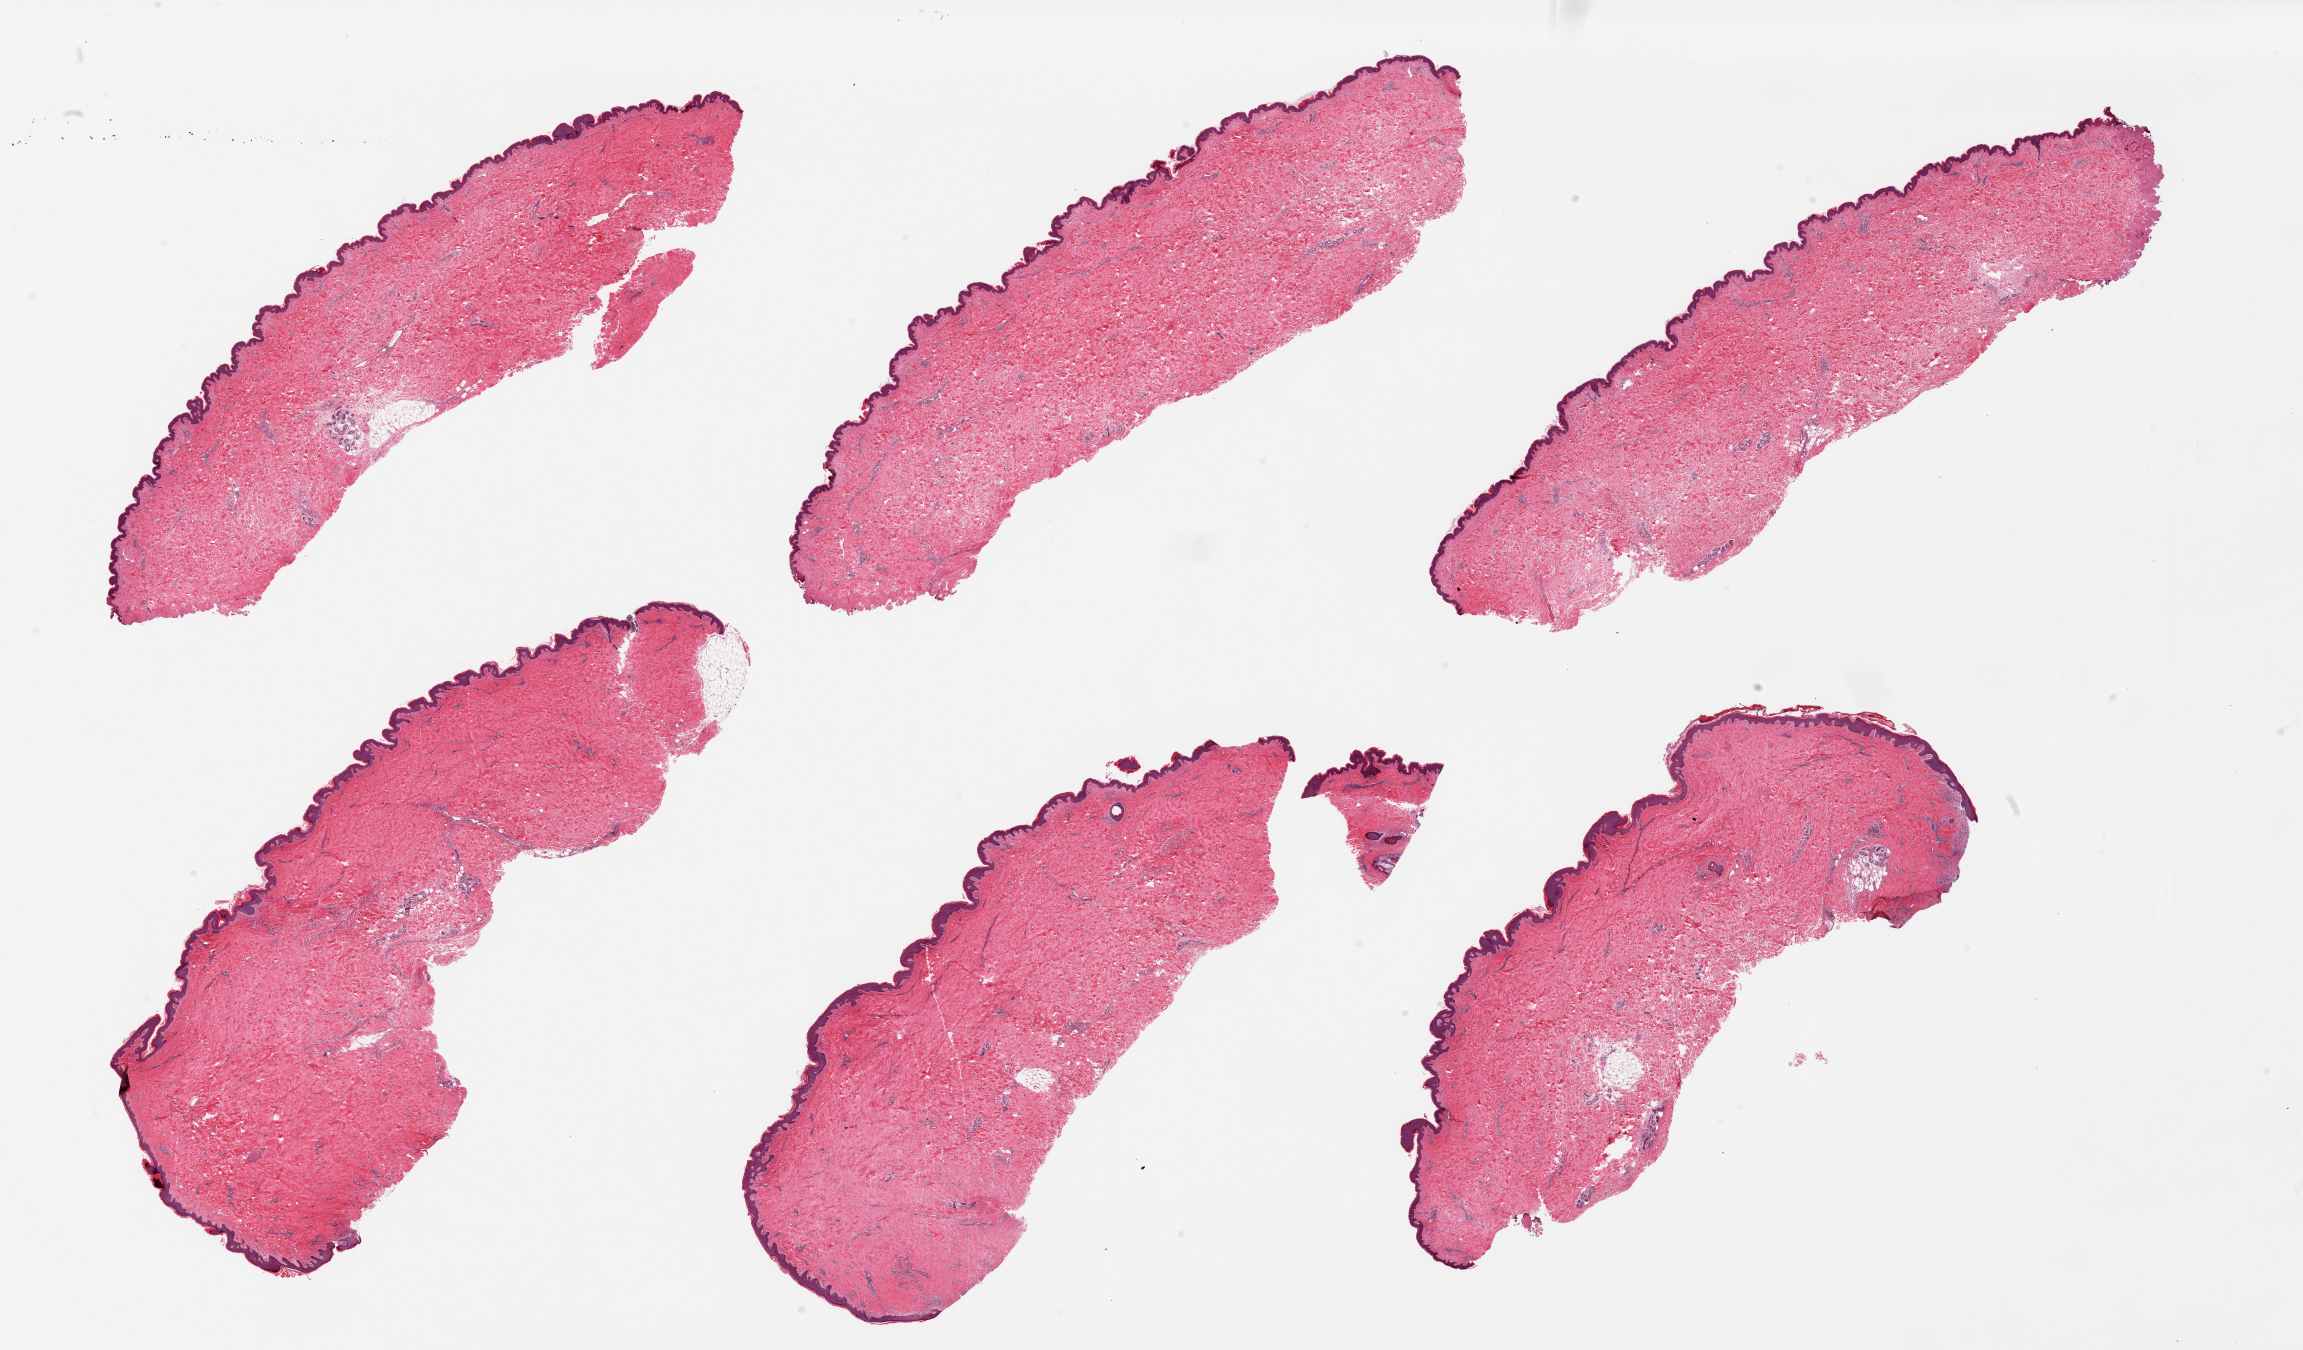
Haematoxylin and eosin whole-slide image, brightfield — a low-resolution overview of the entire scanned area, about 36.4 x 21.4 mm (acquisition: 20x scan), PAXgene-fixed paraffin-embedded (PFPE) section, section of skin of suprapubic region (target tissue), donor tissue sample. Female donor.
Reviewer comment on this tissue sample: 6 pieces, up to 13x4mm; squamous epithelium is ~2% thickness.